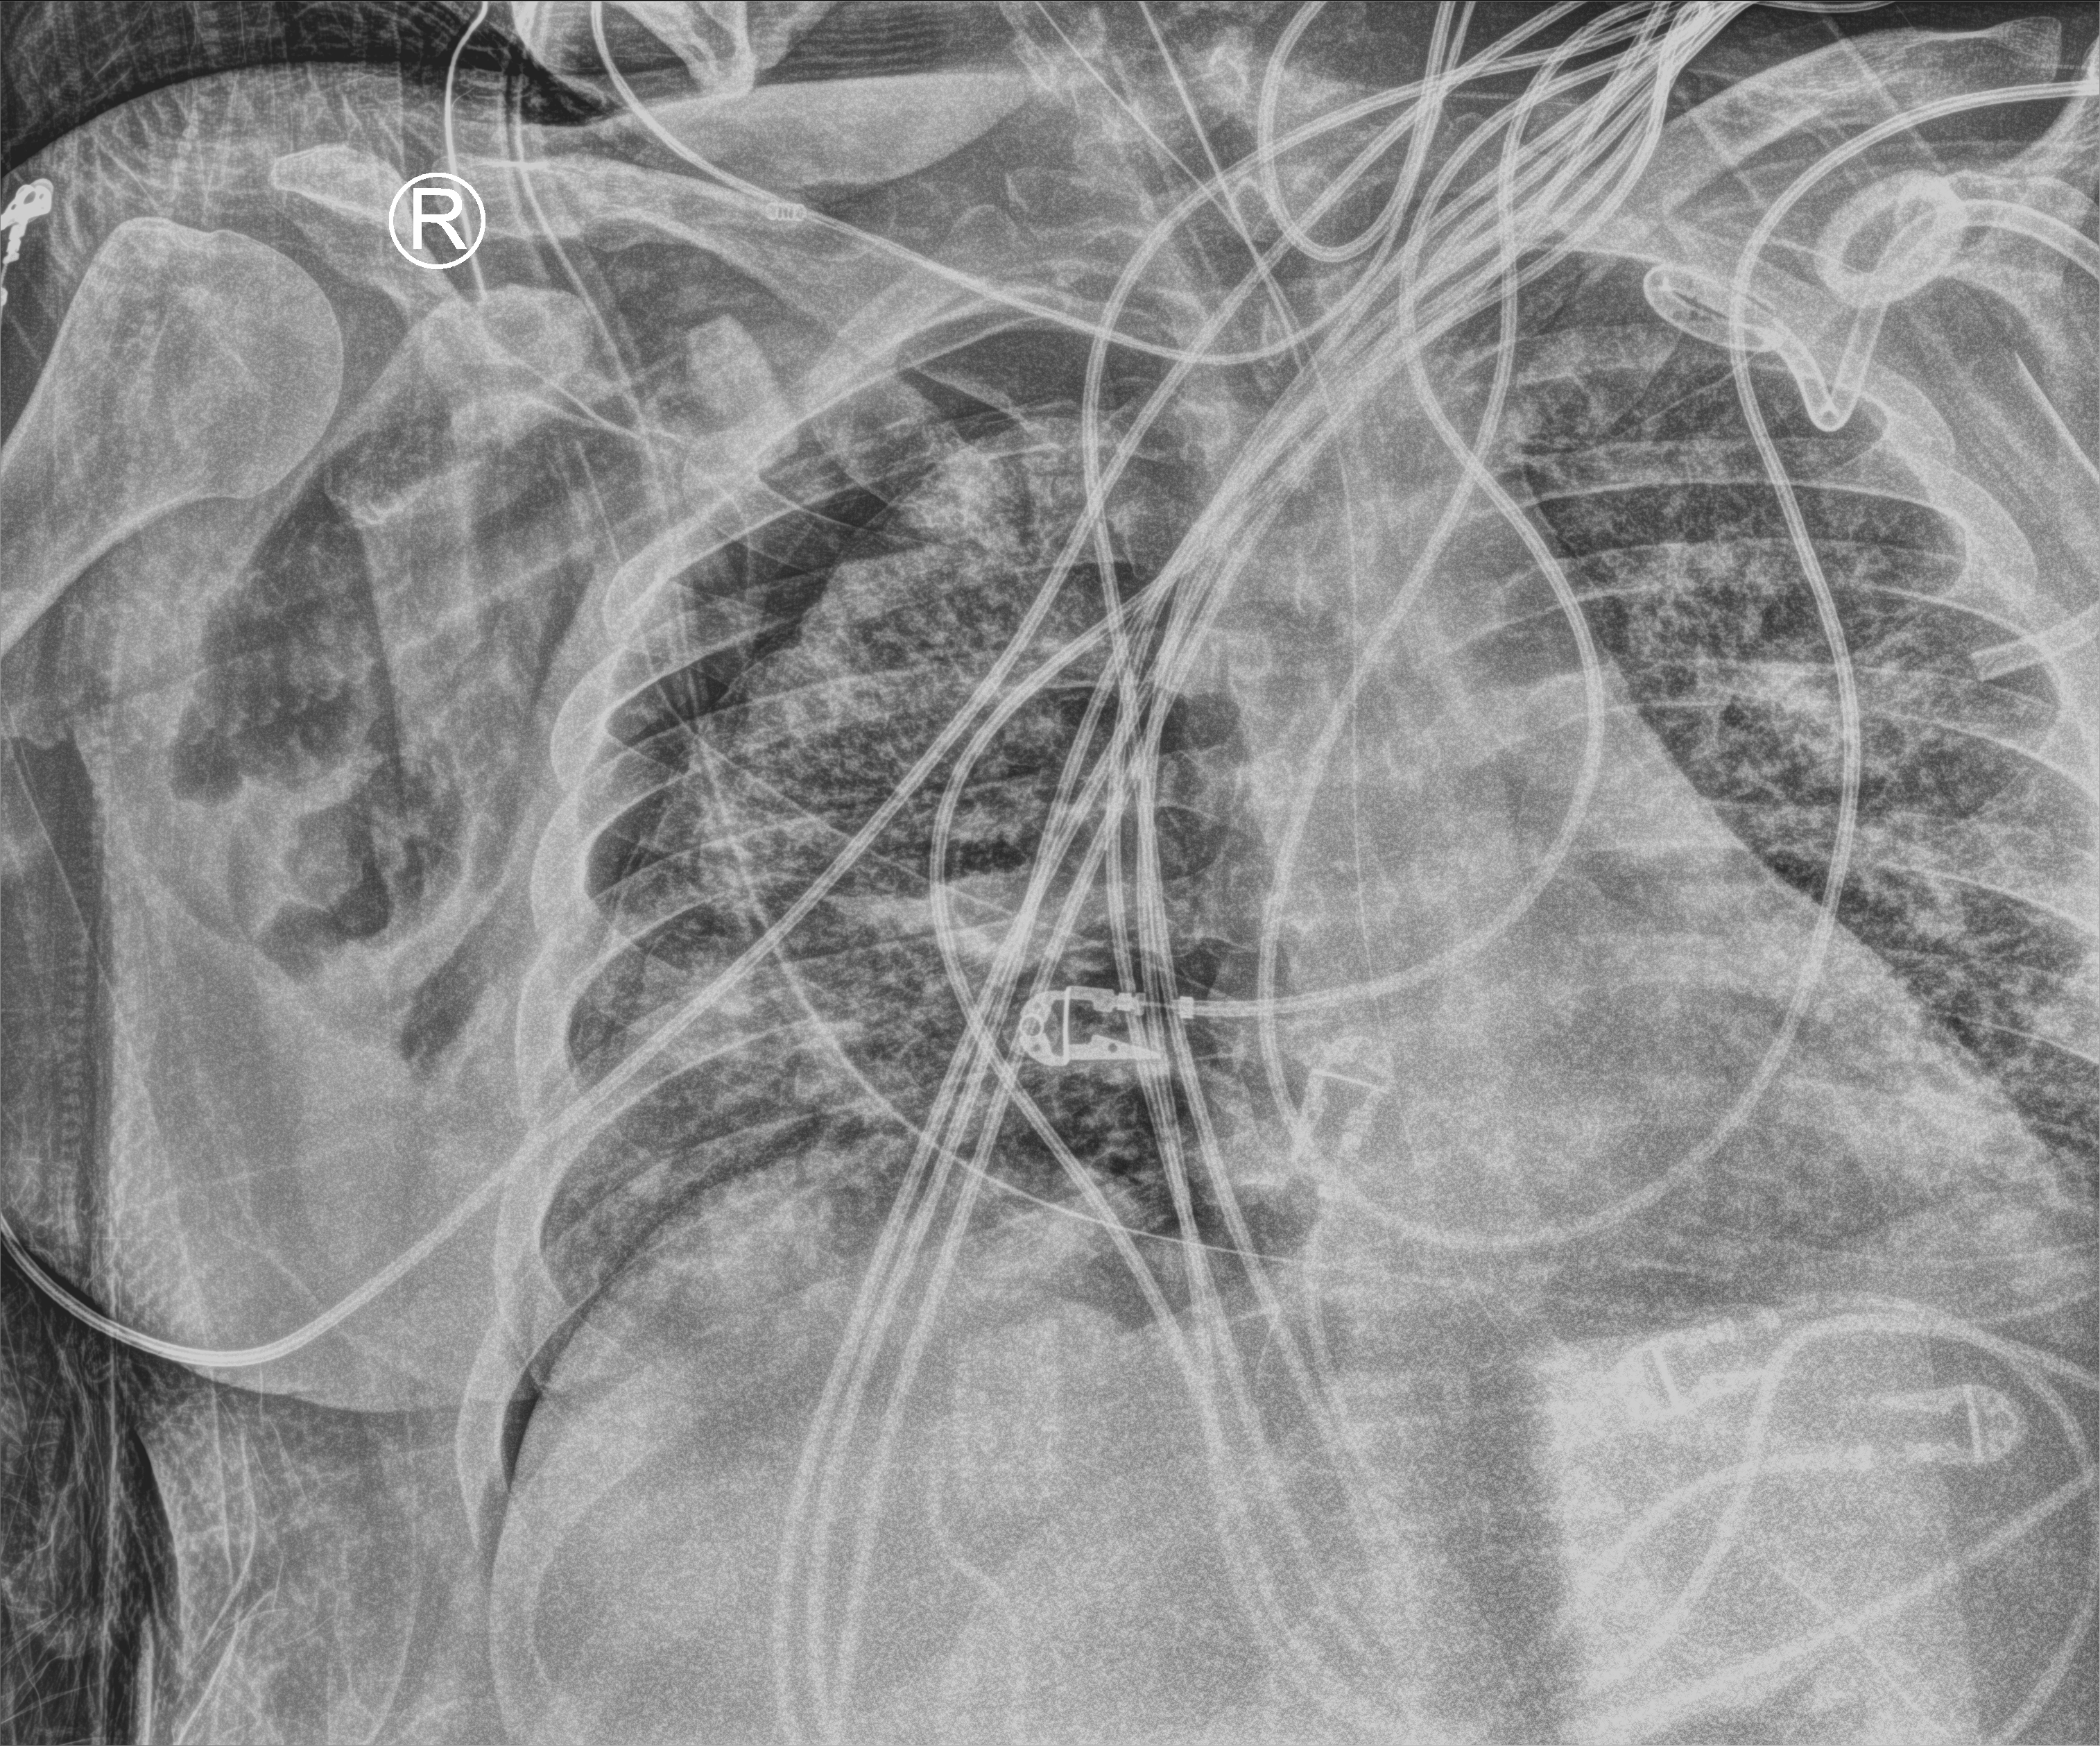
Portable chest radiograph, anteroposterior (AP) projection. Patient hospitalised with COVID-19, aged 18–59 years.
From the hospital-stay record, not from the radiograph (when in the stay this image was taken is not recorded):
- mechanically ventilated during this hospital stay: yes
- admitted to intensive care during this hospital stay: yes